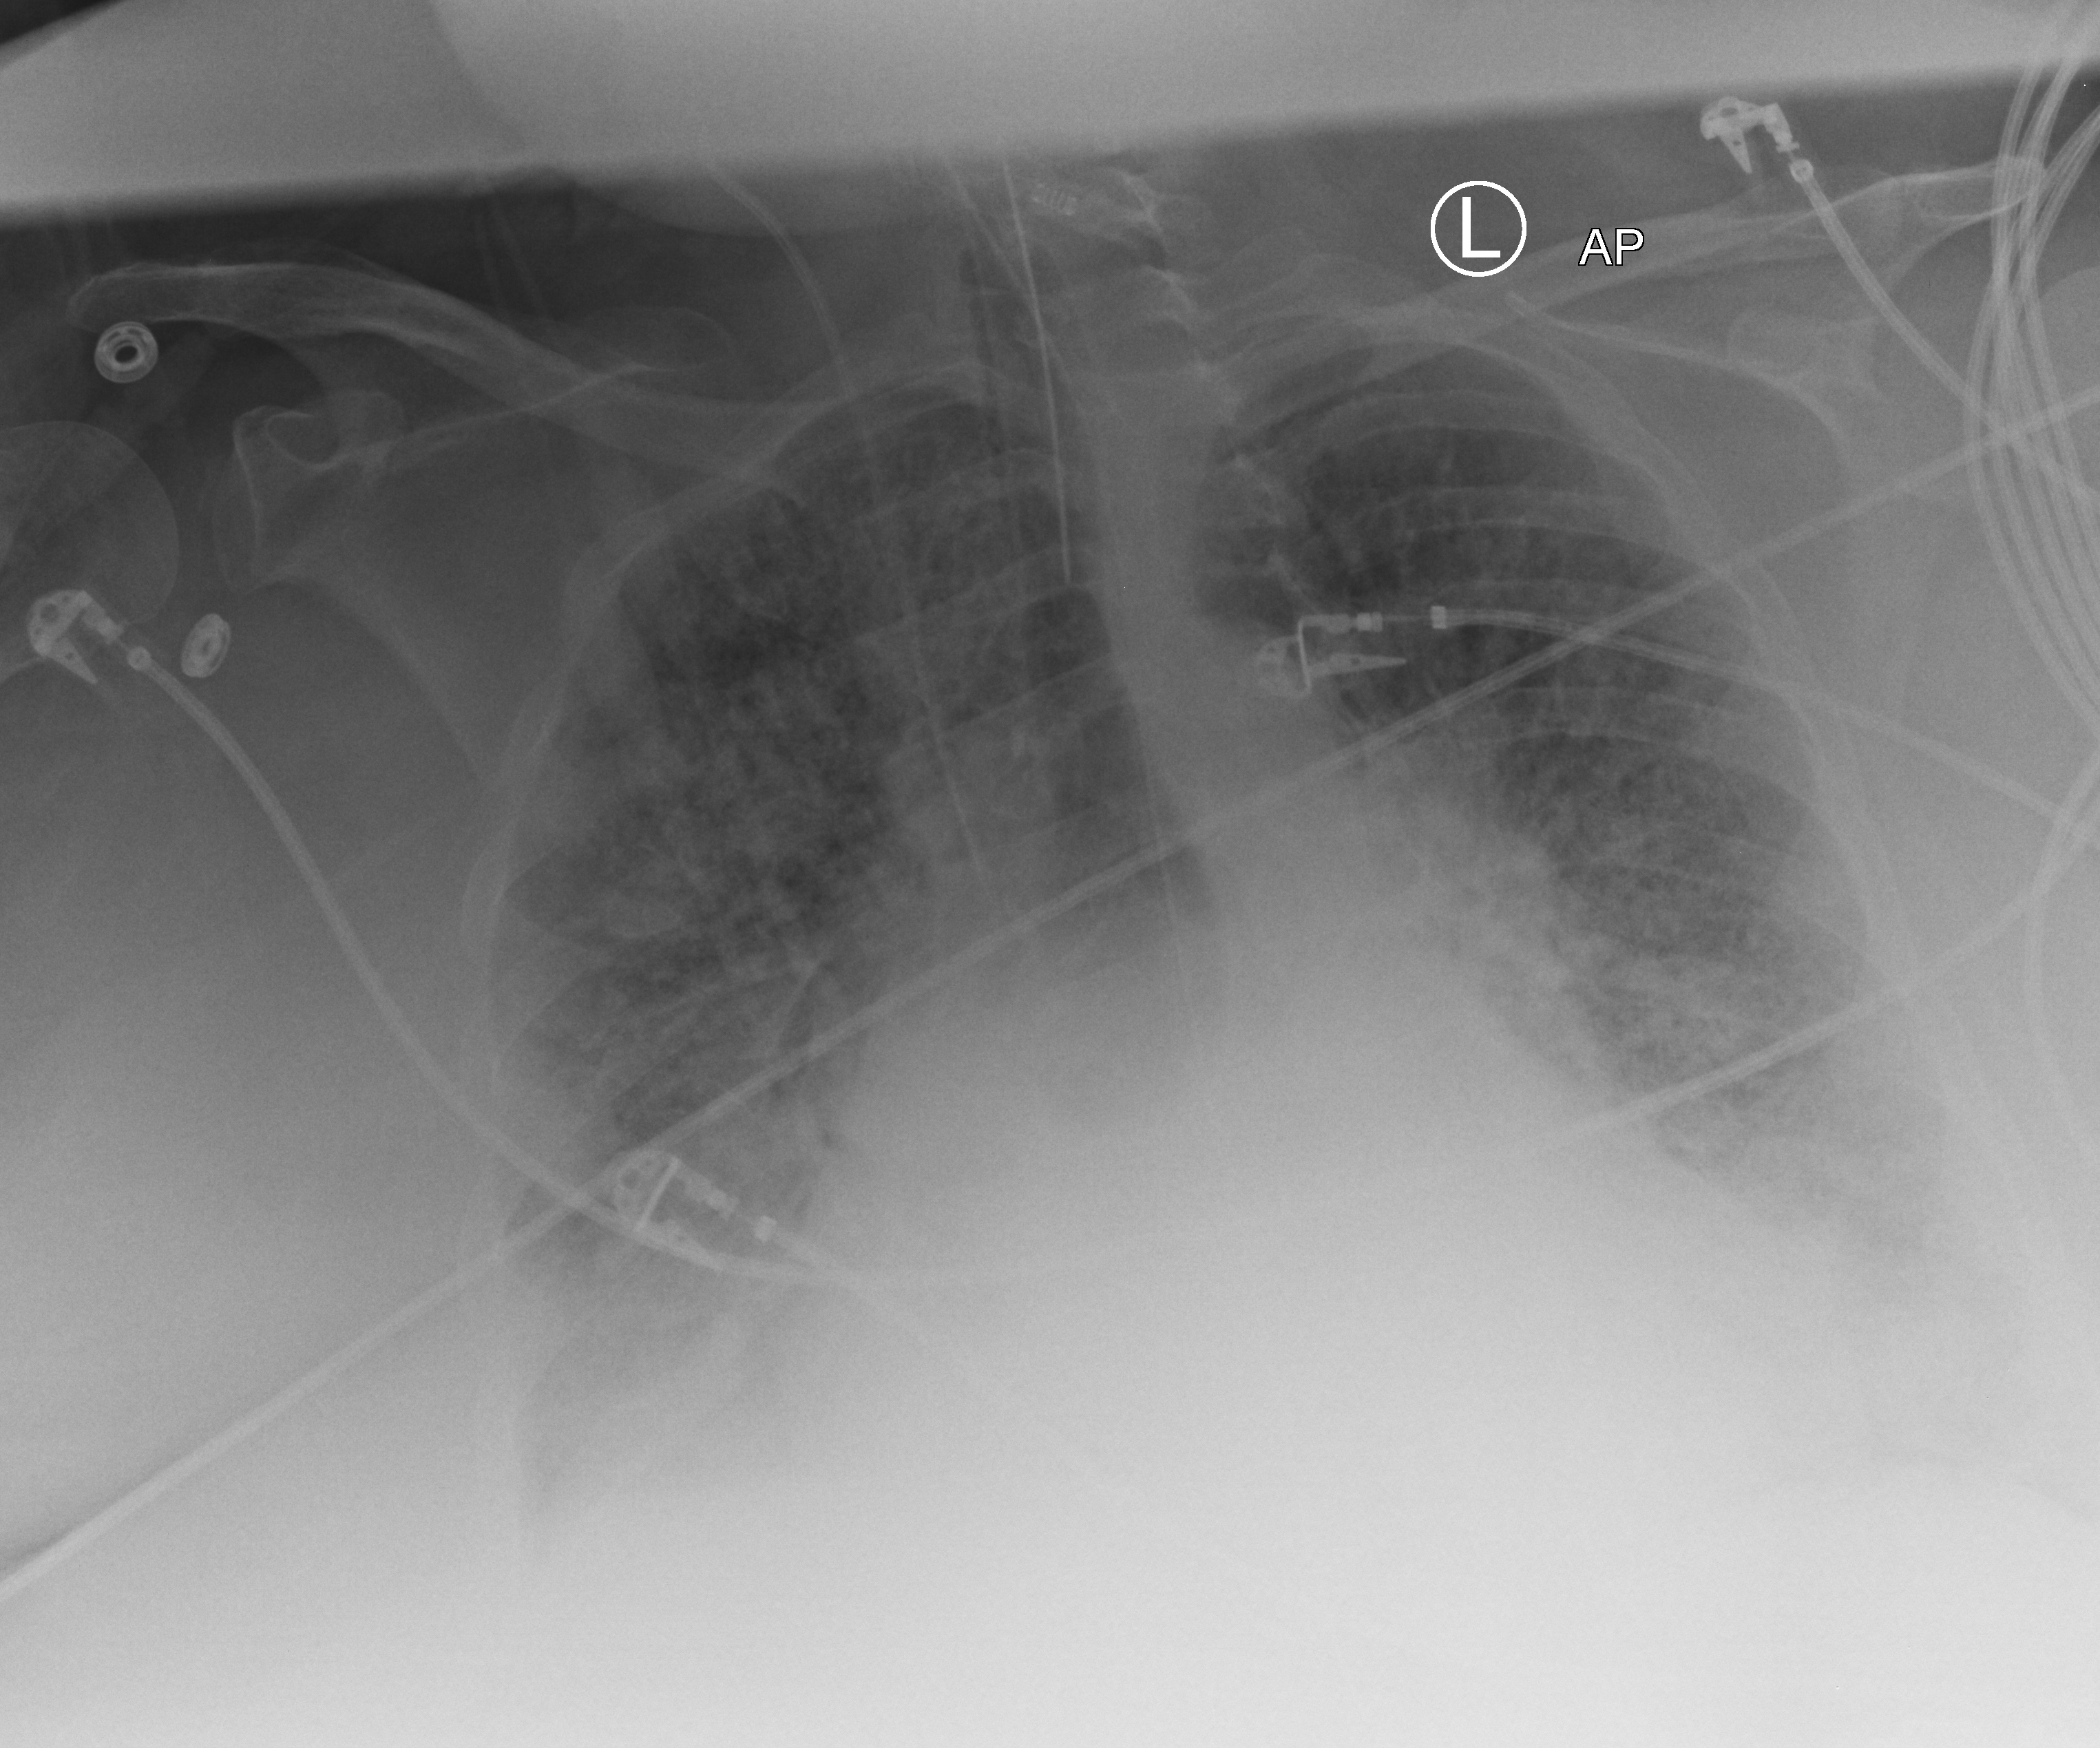
Bedside chest radiograph (computed radiography); anteroposterior (AP) projection. Female patient hospitalised with COVID-19, age 60–74 years.
From the hospital-stay record, not from the radiograph (when in the stay this image was taken is not recorded): admitted to intensive care during this hospital stay: yes; COPD (admission record): yes.